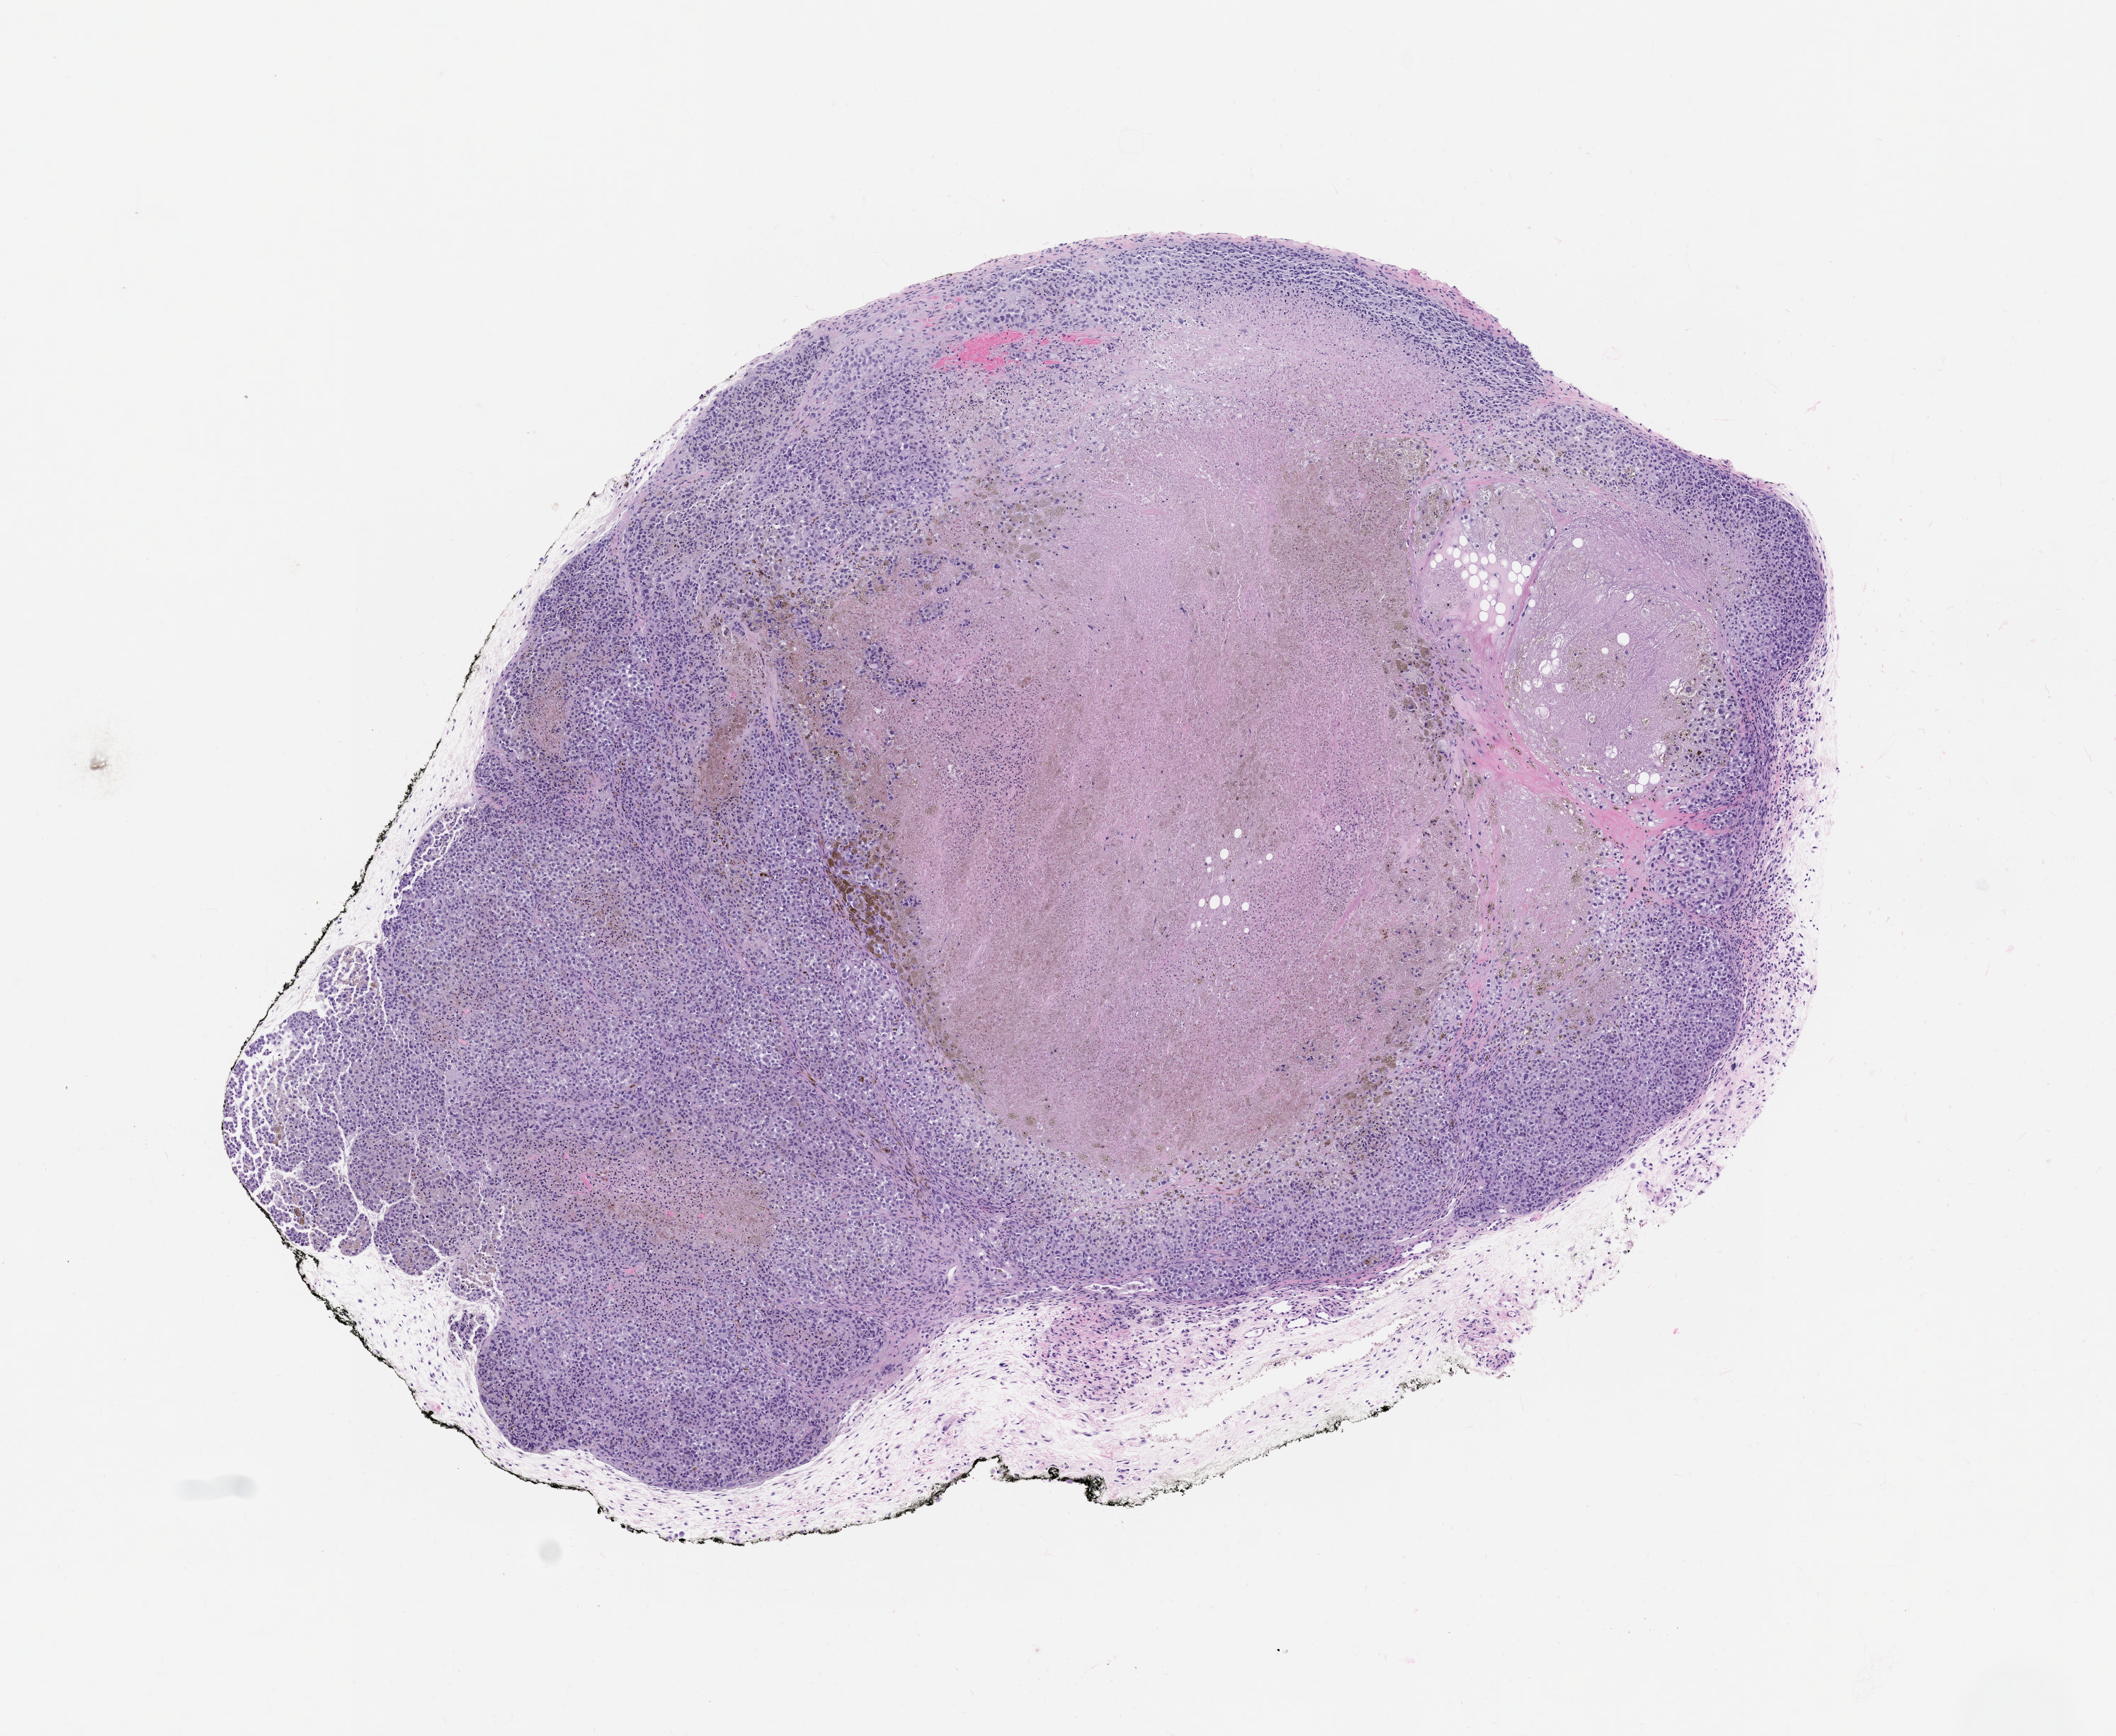
Whole-slide image, haematoxylin and eosin: patient-derived xenograft (human tumor grown in a mouse), passage 0, low-resolution overview of the scanned area, about 6.0 x 4.9 mm, FFPE section, tumor site category: skin.
Originating patient diagnosis: Melanoma.